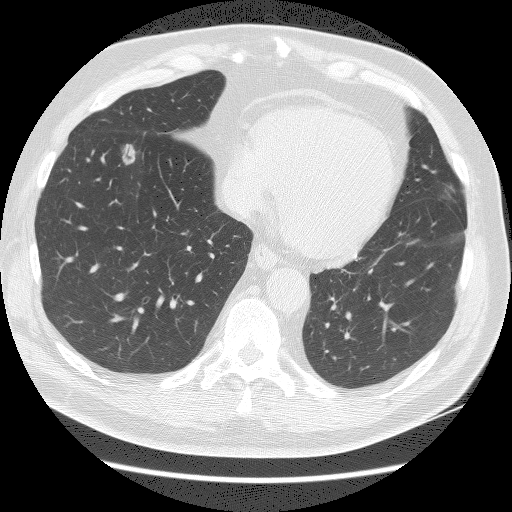
Axial slice from a low-dose chest CT screening exam, baseline annual screen, lung window (W 1500 / L -600 HU), 2.5 mm slice thickness, lung (sharp) reconstruction kernel (BONE). Male participant, aged 65 years at enrolment.
- Expert-annotated lung lesion, box from (x=104, y=133) to (x=151, y=171) px.
- The screening reader recorded 3 non-calcified nodules or masses ≥4 mm on this exam; which of them this box marks is not recorded.
- Official screen result: positive, change unspecified: nodule(s) >= 4 mm or enlarging nodule(s), mass(es), or other non-specific abnormalities suspicious for lung cancer.
- Participant outcome: lung cancer diagnosed 132 days after this screen — adenocarcinoma, NOS, right lower lobe, poorly differentiated (G3), stage IA (AJCC 6th edition), 10 mm at pathology.